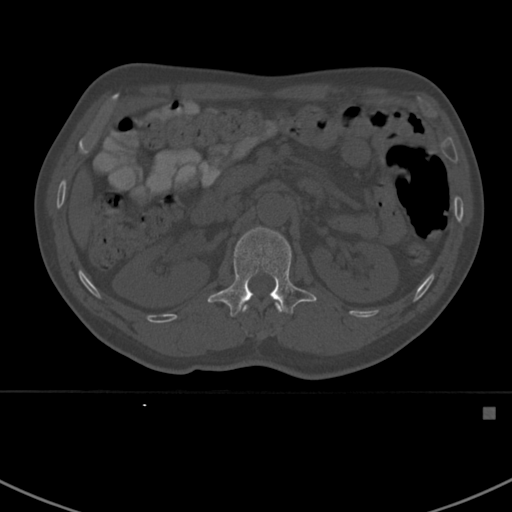
CT including the spine, one axial slice; reconstruction kernel Br40s; 120 kVp; bone window (W 1800 / L 400 HU); 512 × 512 image matrix, field of view 358 × 358 mm. Patient: male, 59 years. Case-level facts recorded for this patient, not image findings: primary cancer: prostate.
Structures marked on this image (semi-automatic segmentation, software-assisted and operator-edited):
- L1 vertebra: bounding box (x1, y1, x2, y2) in pixels: (207, 225, 317, 317)
- T12 vertebra: (243, 304, 280, 312)